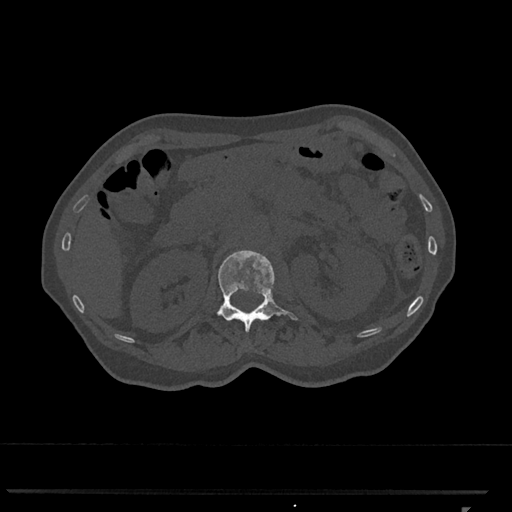
CT including the spine, one axial slice; position 402 of 793 along the scan axis; reconstruction kernel Br40s/3; bone window (W 1800 / L 400 HU); 0.5 mm slice thickness; 512 × 512 image matrix. Female patient, age 62 years. From the clinical record (not read from this slice): primary cancer: renal.
Structures marked on this image (semi-automatic segmentation, software-assisted and operator-edited):
- L1 vertebra: bounding box <217,250,298,333> (left, top, right, bottom; pixels)